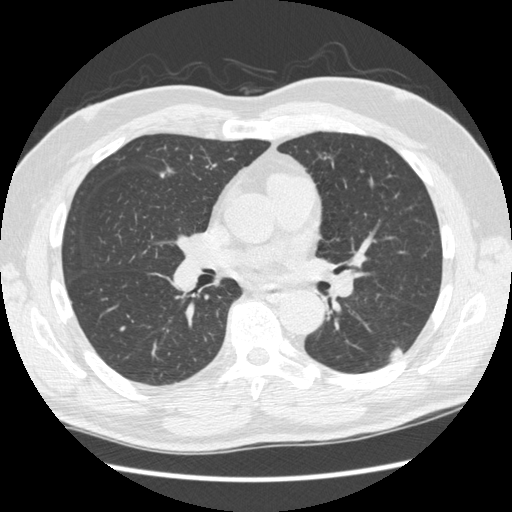
Low-dose screening chest CT, axial slice, first (baseline) screen, lung window (W 1500 / L -600 HU), standard (soft-tissue) reconstruction kernel (STANDARD). Male participant, aged 74 years at enrolment. Former smoker at enrolment.
Expert-annotated lung lesion, bounding box (x1, y1, x2, y2) in pixels: (372, 324, 414, 368). The screening reader recorded 3 non-calcified nodules or masses ≥4 mm on this exam (right upper lobe, right lower lobe, left upper lobe); which of them this box marks is not recorded. Official screen result: positive, change unspecified: nodule(s) >= 4 mm or enlarging nodule(s), mass(es), or other non-specific abnormalities suspicious for lung cancer. Lung cancer was diagnosed 384 days after this screen (after the second annual screen): squamous cell carcinoma, NOS, left lower lobe, well differentiated (G1), stage IA (AJCC 6th edition), 28 mm at pathology.